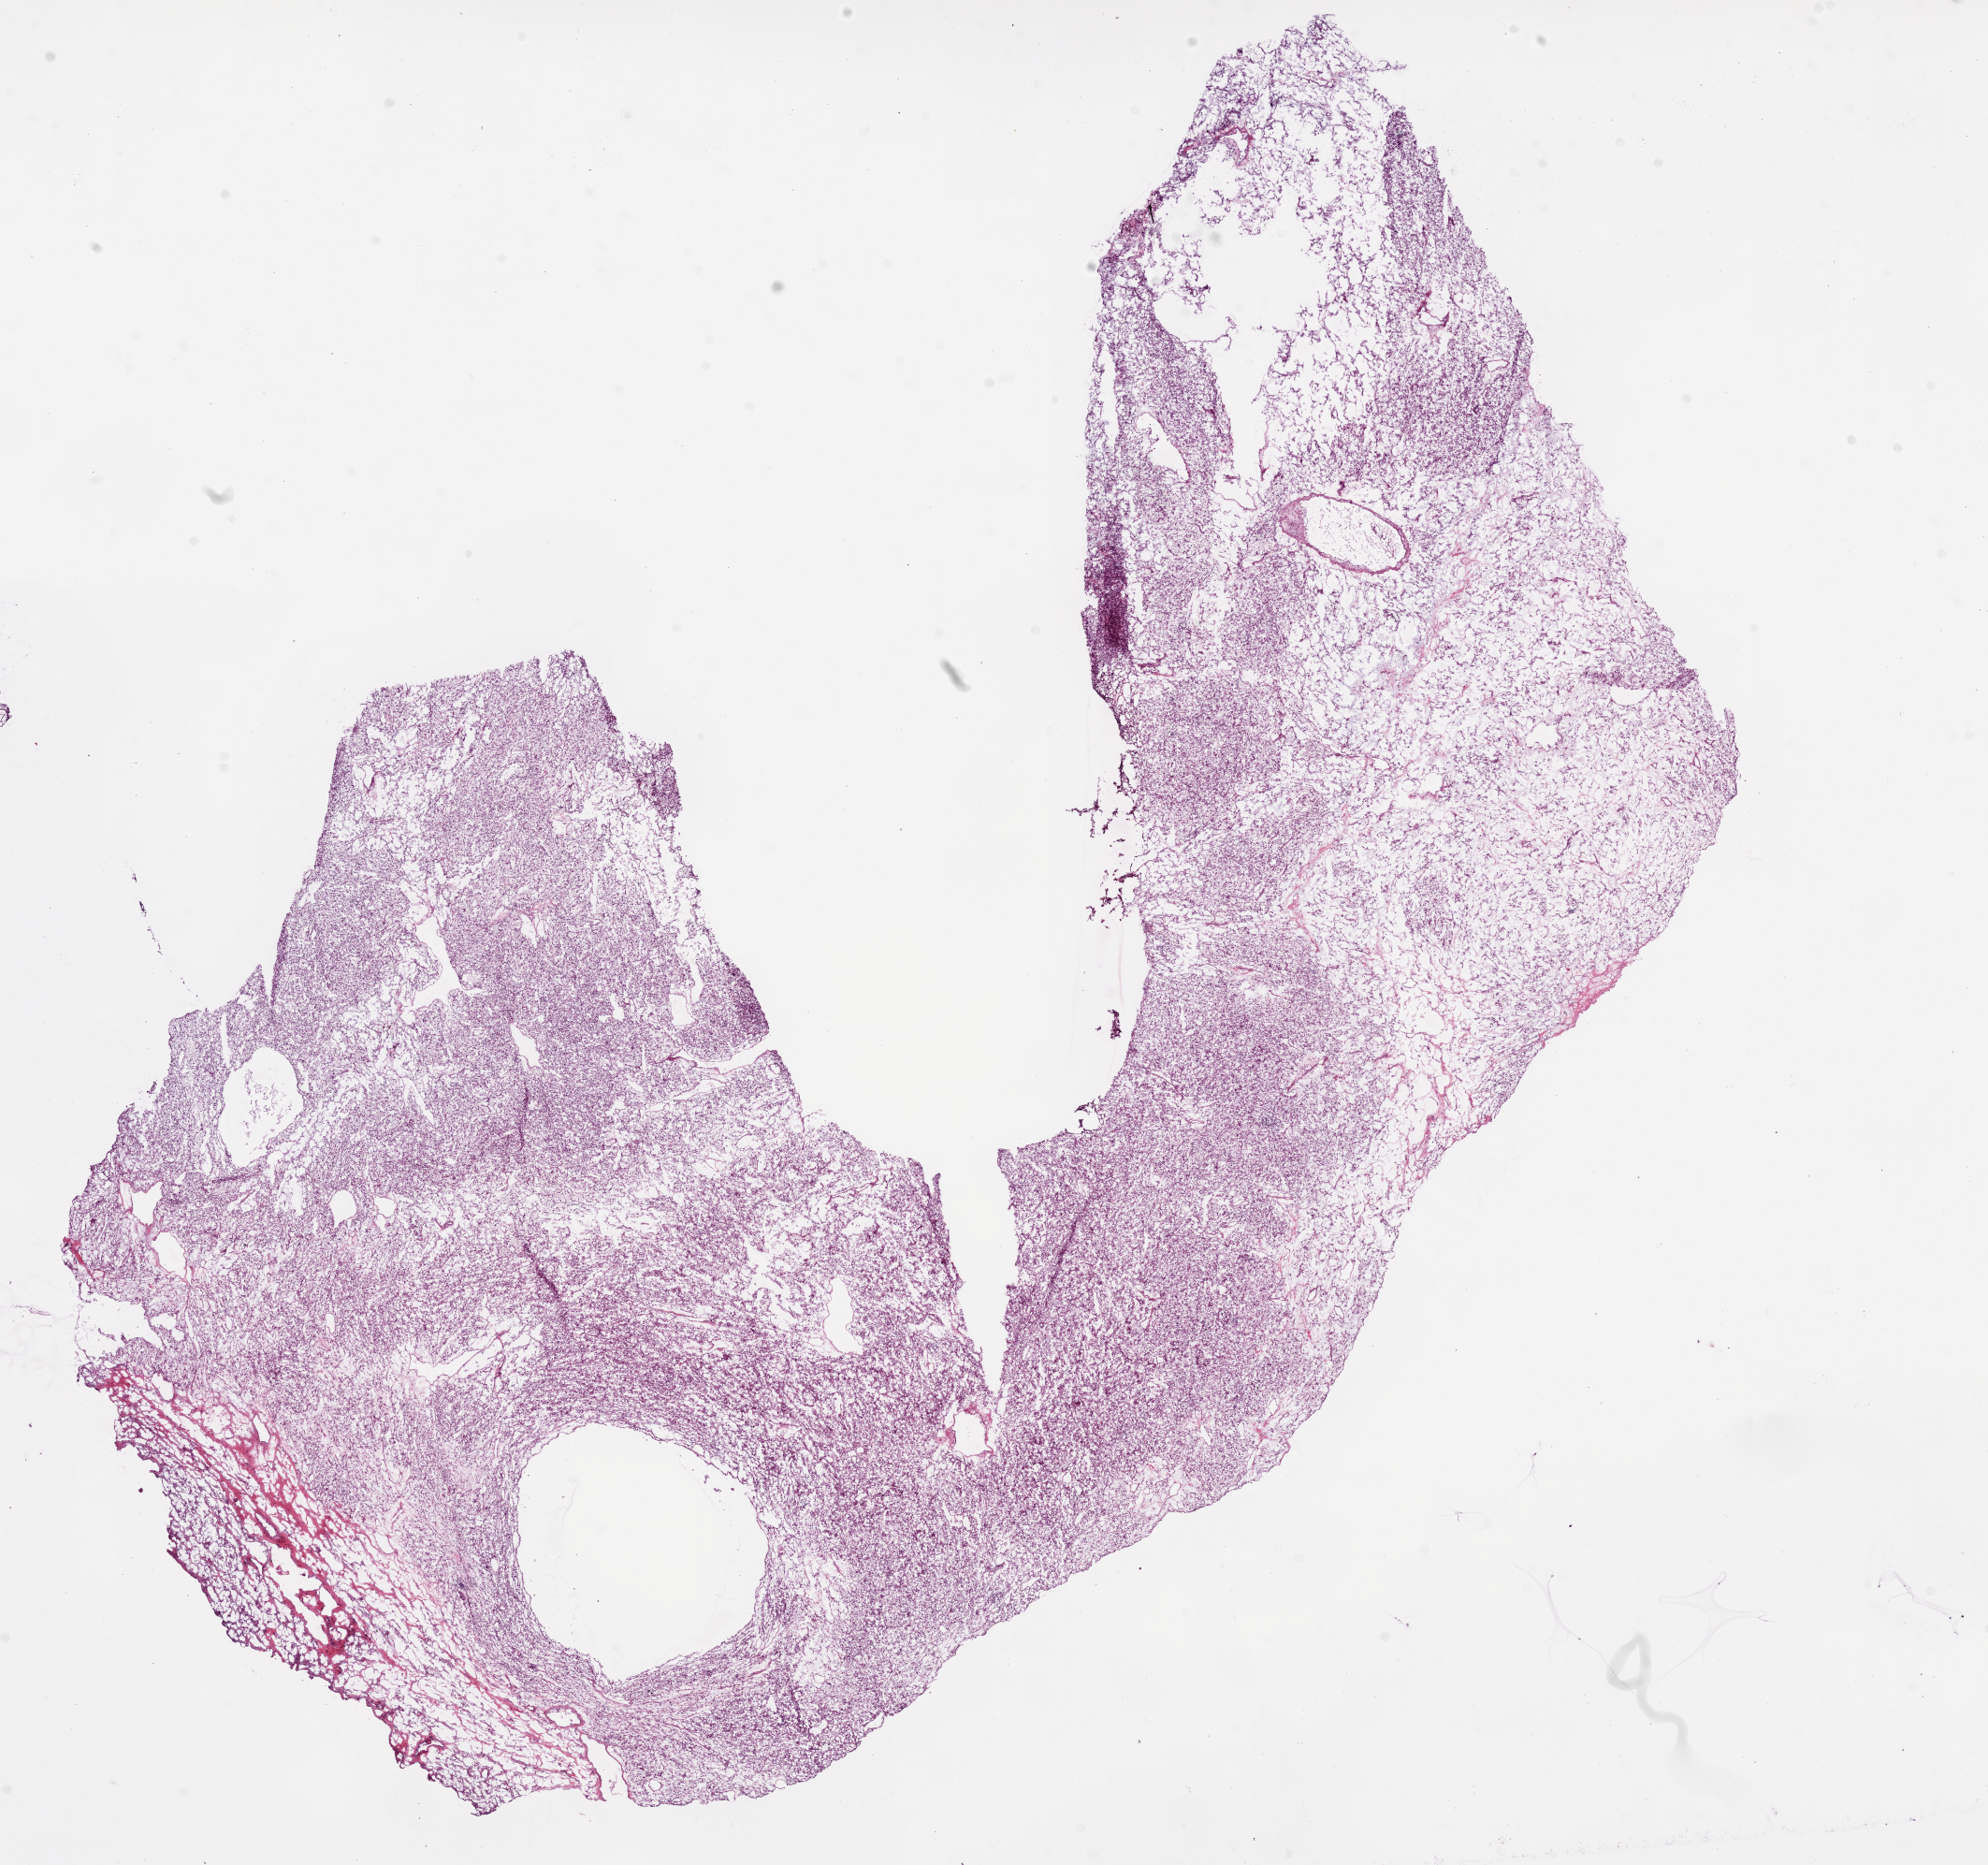
H&E whole-slide image, whole scanned area (about 17.1 x 16.0 mm, acquisition: 20x scan) shown as a low-resolution overview. Frozen section. Sample: primary tumour, kidney. Patient: female, age at initial diagnosis 62 years. Histologic grade: G2 (moderately differentiated). Pathologist review of this section (percent, as recorded): tumour cells 85%, tumour nuclei 85%, normal cells 0%, stromal cells 15%, necrosis 0%.
* diagnosis: Clear cell adenocarcinoma, NOS
* laterality: left
* lymph nodes positive (case pathology): 0 of 4 examined
* AJCC pathologic stage: I